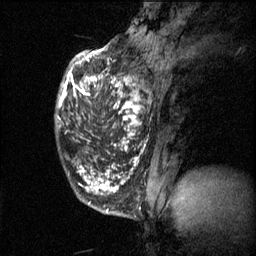
Breast MRI (dynamic contrast-enhanced), one sagittal slice. Slice 16 of 60 in the series (ordered by position). 3 images stored at this slice position (order not interpretable as contrast timing). 1.5 T. TE 4.2 ms, TR 11.1 ms. 2 mm slice thickness. 256 × 256 image matrix, field of view 180 × 180 mm. Female patient, age 50 years.
Outlined on this slice (semi-automatic segmentation, software-assisted and operator-edited):
- analysis volume of interest (the breast-tissue region the enhancement analysis was run in; not a lesion): bounding box <82,68,153,141> (left, top, right, bottom; pixels)
- tumour enhancement mask (voxels above the 70 % enhancement threshold inside the analysis volume of interest): <82,68,145,139>